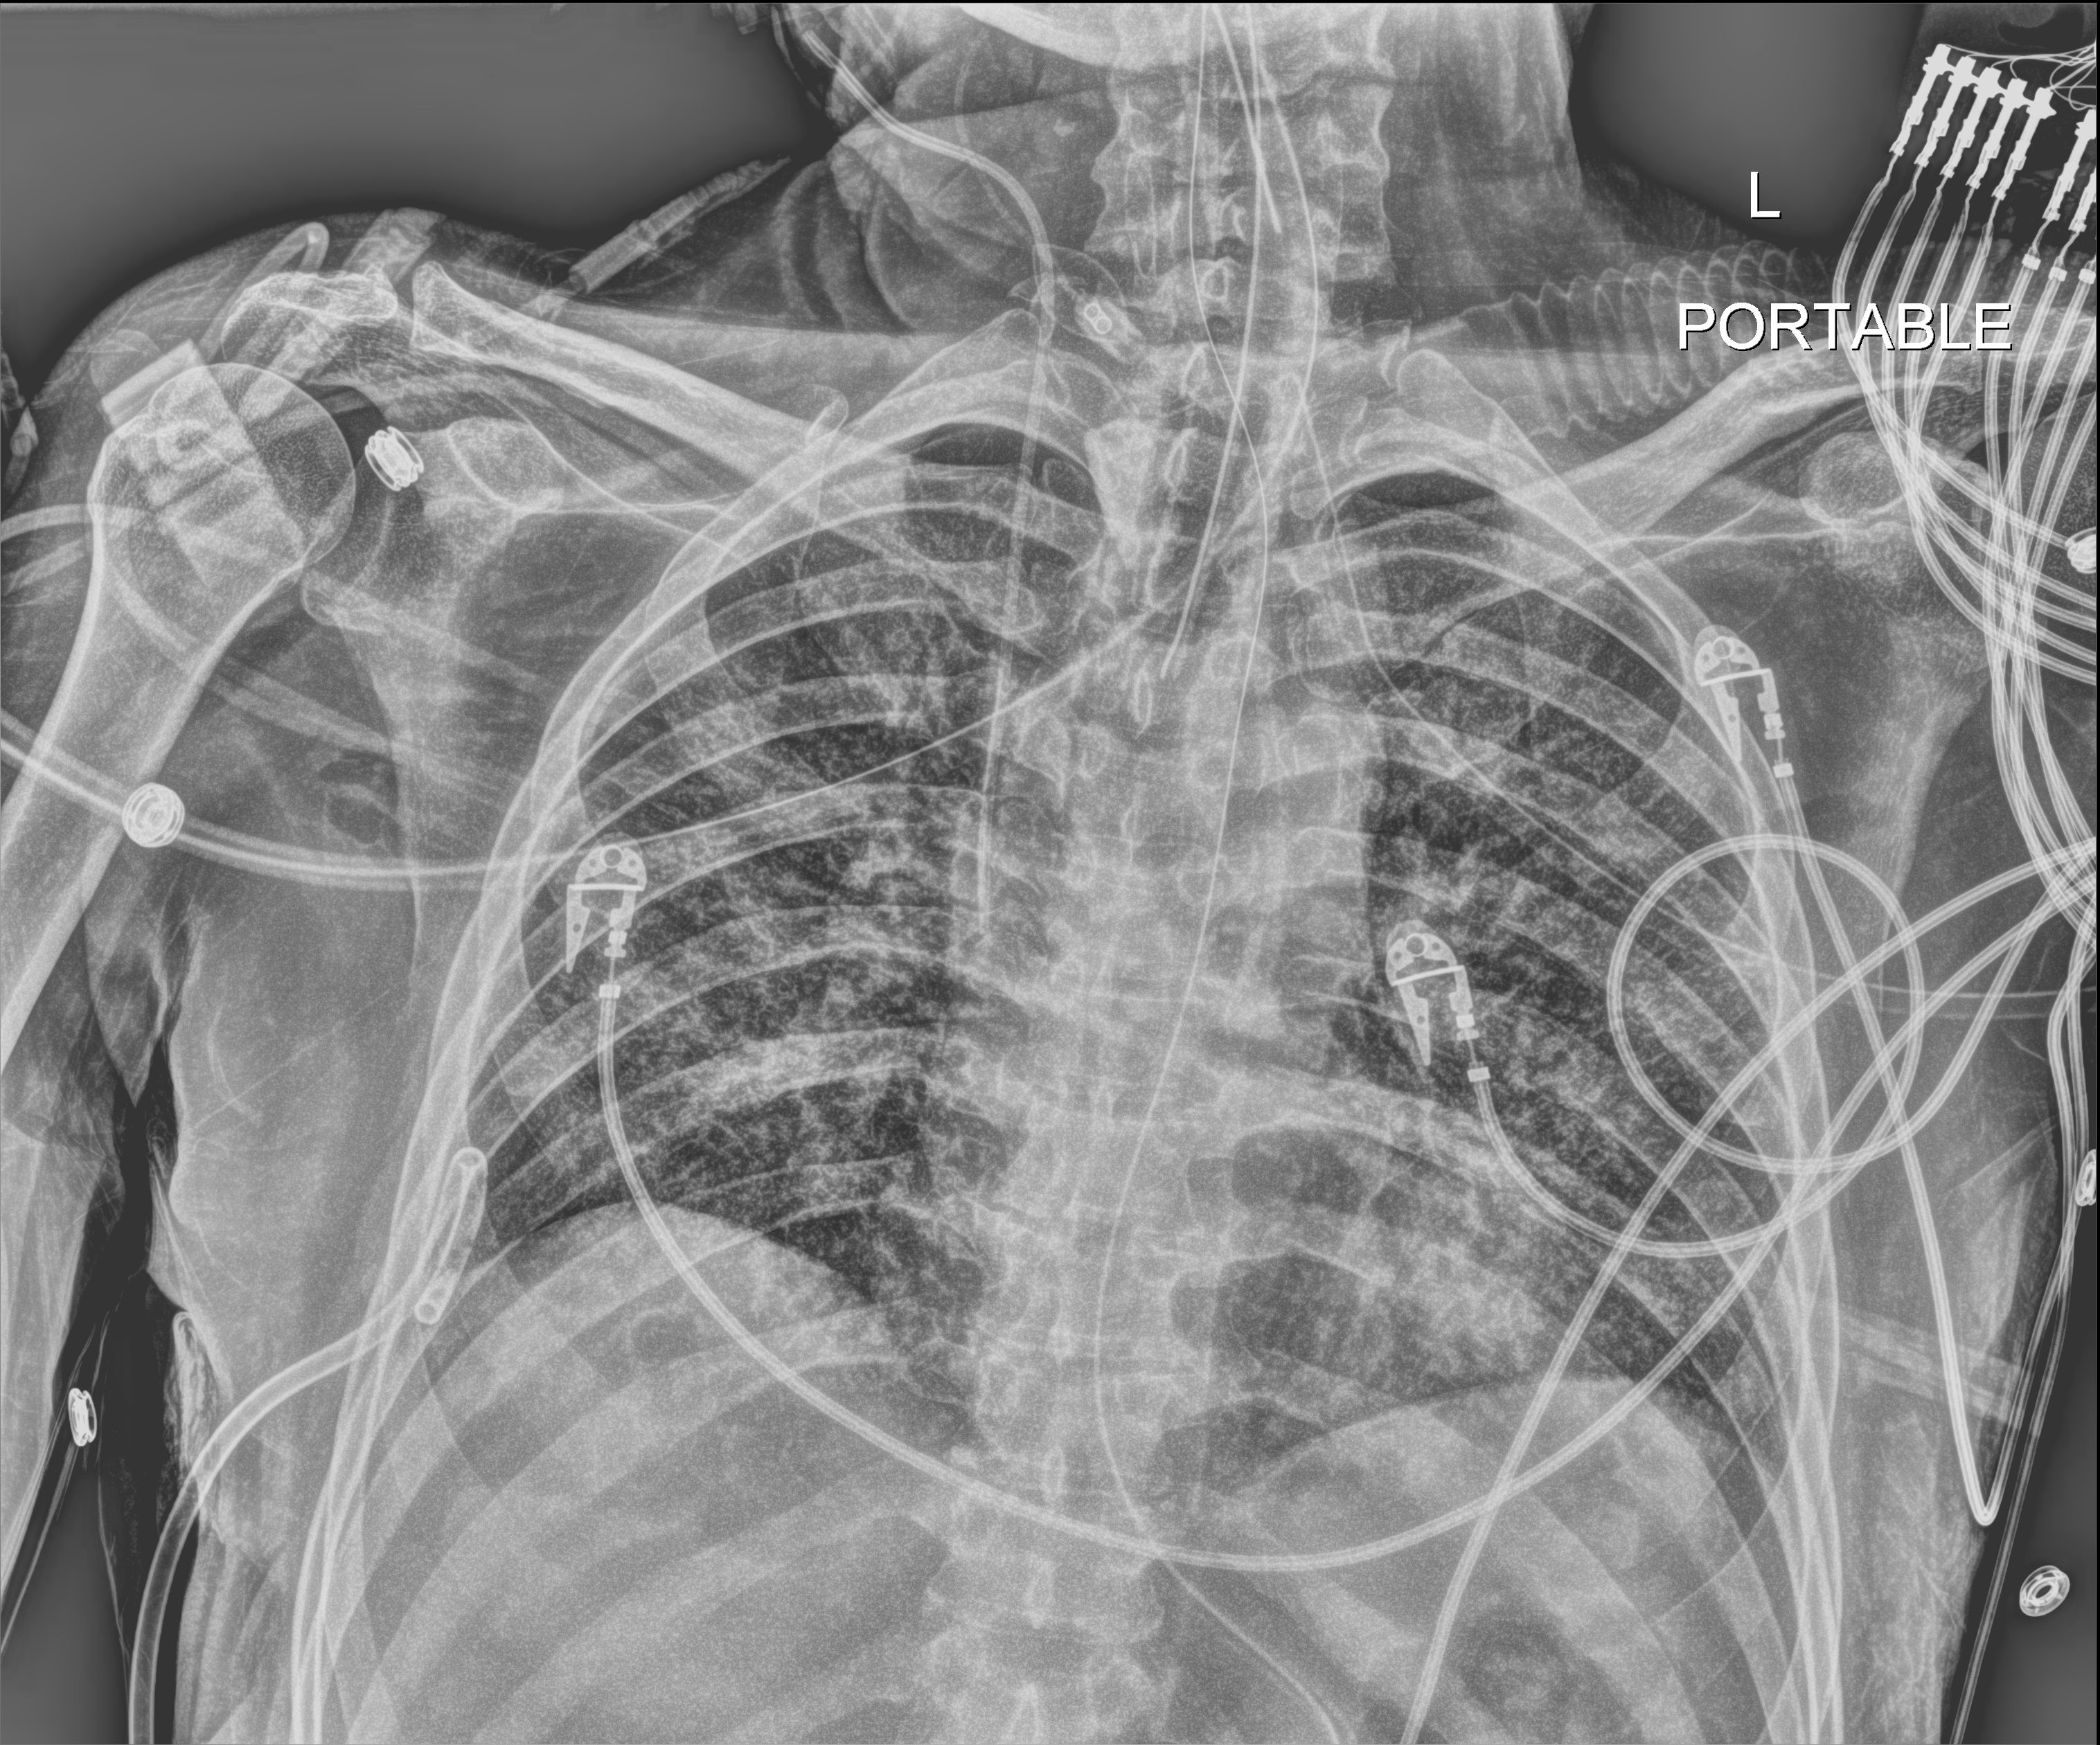
Portable chest radiograph, anteroposterior (AP) projection. Male patient hospitalised with COVID-19, age 18–59 years.
Hospital-stay facts (about this admission, not read from this image; timing relative to this image not recorded):
- mechanically ventilated during this hospital stay: yes
- smoking status (admission record): never